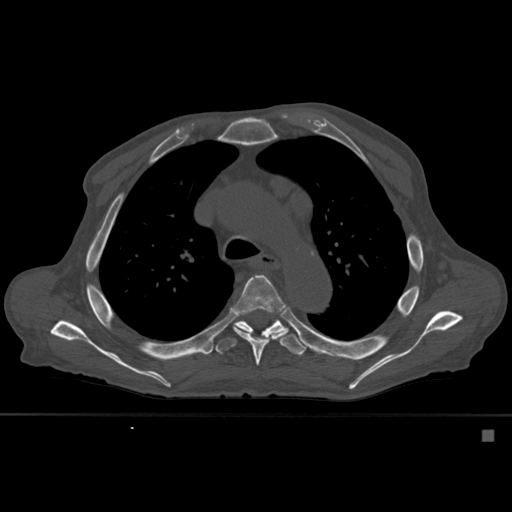
CT including the spine, one axial slice; position 396 of 527 along the scan axis; bone window (W 1800 / L 400 HU); 1.5 mm slice thickness; 512 × 512 image matrix, field of view 373 × 373 mm. Patient: male, 78 years. From the clinical record (not read from this slice): primary cancer: prostate.
Annotated regions visible in this slice (semi-automatically segmented with operator editing):
- T5 vertebra: bounding box (x1, y1, x2, y2) in pixels: (235, 274, 285, 366)
- T6 vertebra: (215, 318, 306, 356)